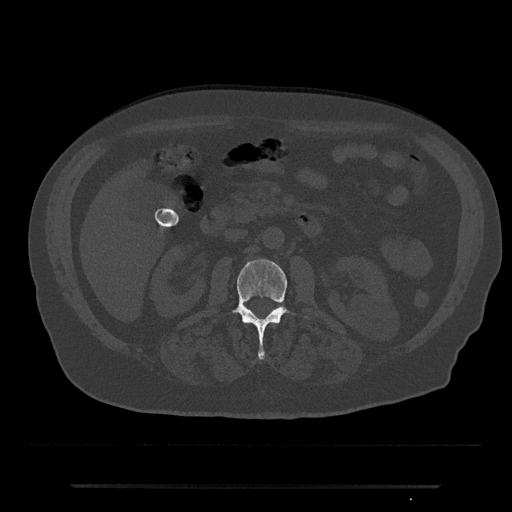
CT including the spine, one axial slice; bone window (W 1800 / L 400 HU); 512 × 512 image matrix. Patient: male, 80 years. From the clinical record (not read from this slice): primary cancer: prostate; vertebrae with lytic lesions (as recorded): L1, T11.
Annotated regions visible in this slice (semi-automatically segmented with operator editing):
- L2 vertebra: bounding box <233,259,289,361> (left, top, right, bottom; pixels)